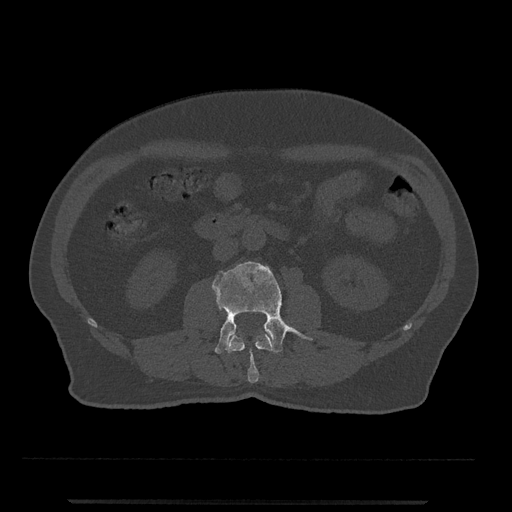
CT including the spine, one axial slice. Position 225 of 797 along the scan axis. Bone window (W 1800 / L 400 HU). 0.5 mm slice thickness. 512 × 512 image matrix, field of view 419 × 419 mm. Male patient, age 63 years. Case-level facts recorded for this patient, not image findings: primary cancer: prostate.
Outlined on this slice (semi-automatically segmented with operator editing):
- L2 vertebra: bounding box (x1, y1, x2, y2) in pixels: (227, 333, 274, 383)
- L3 vertebra: (212, 261, 312, 354)